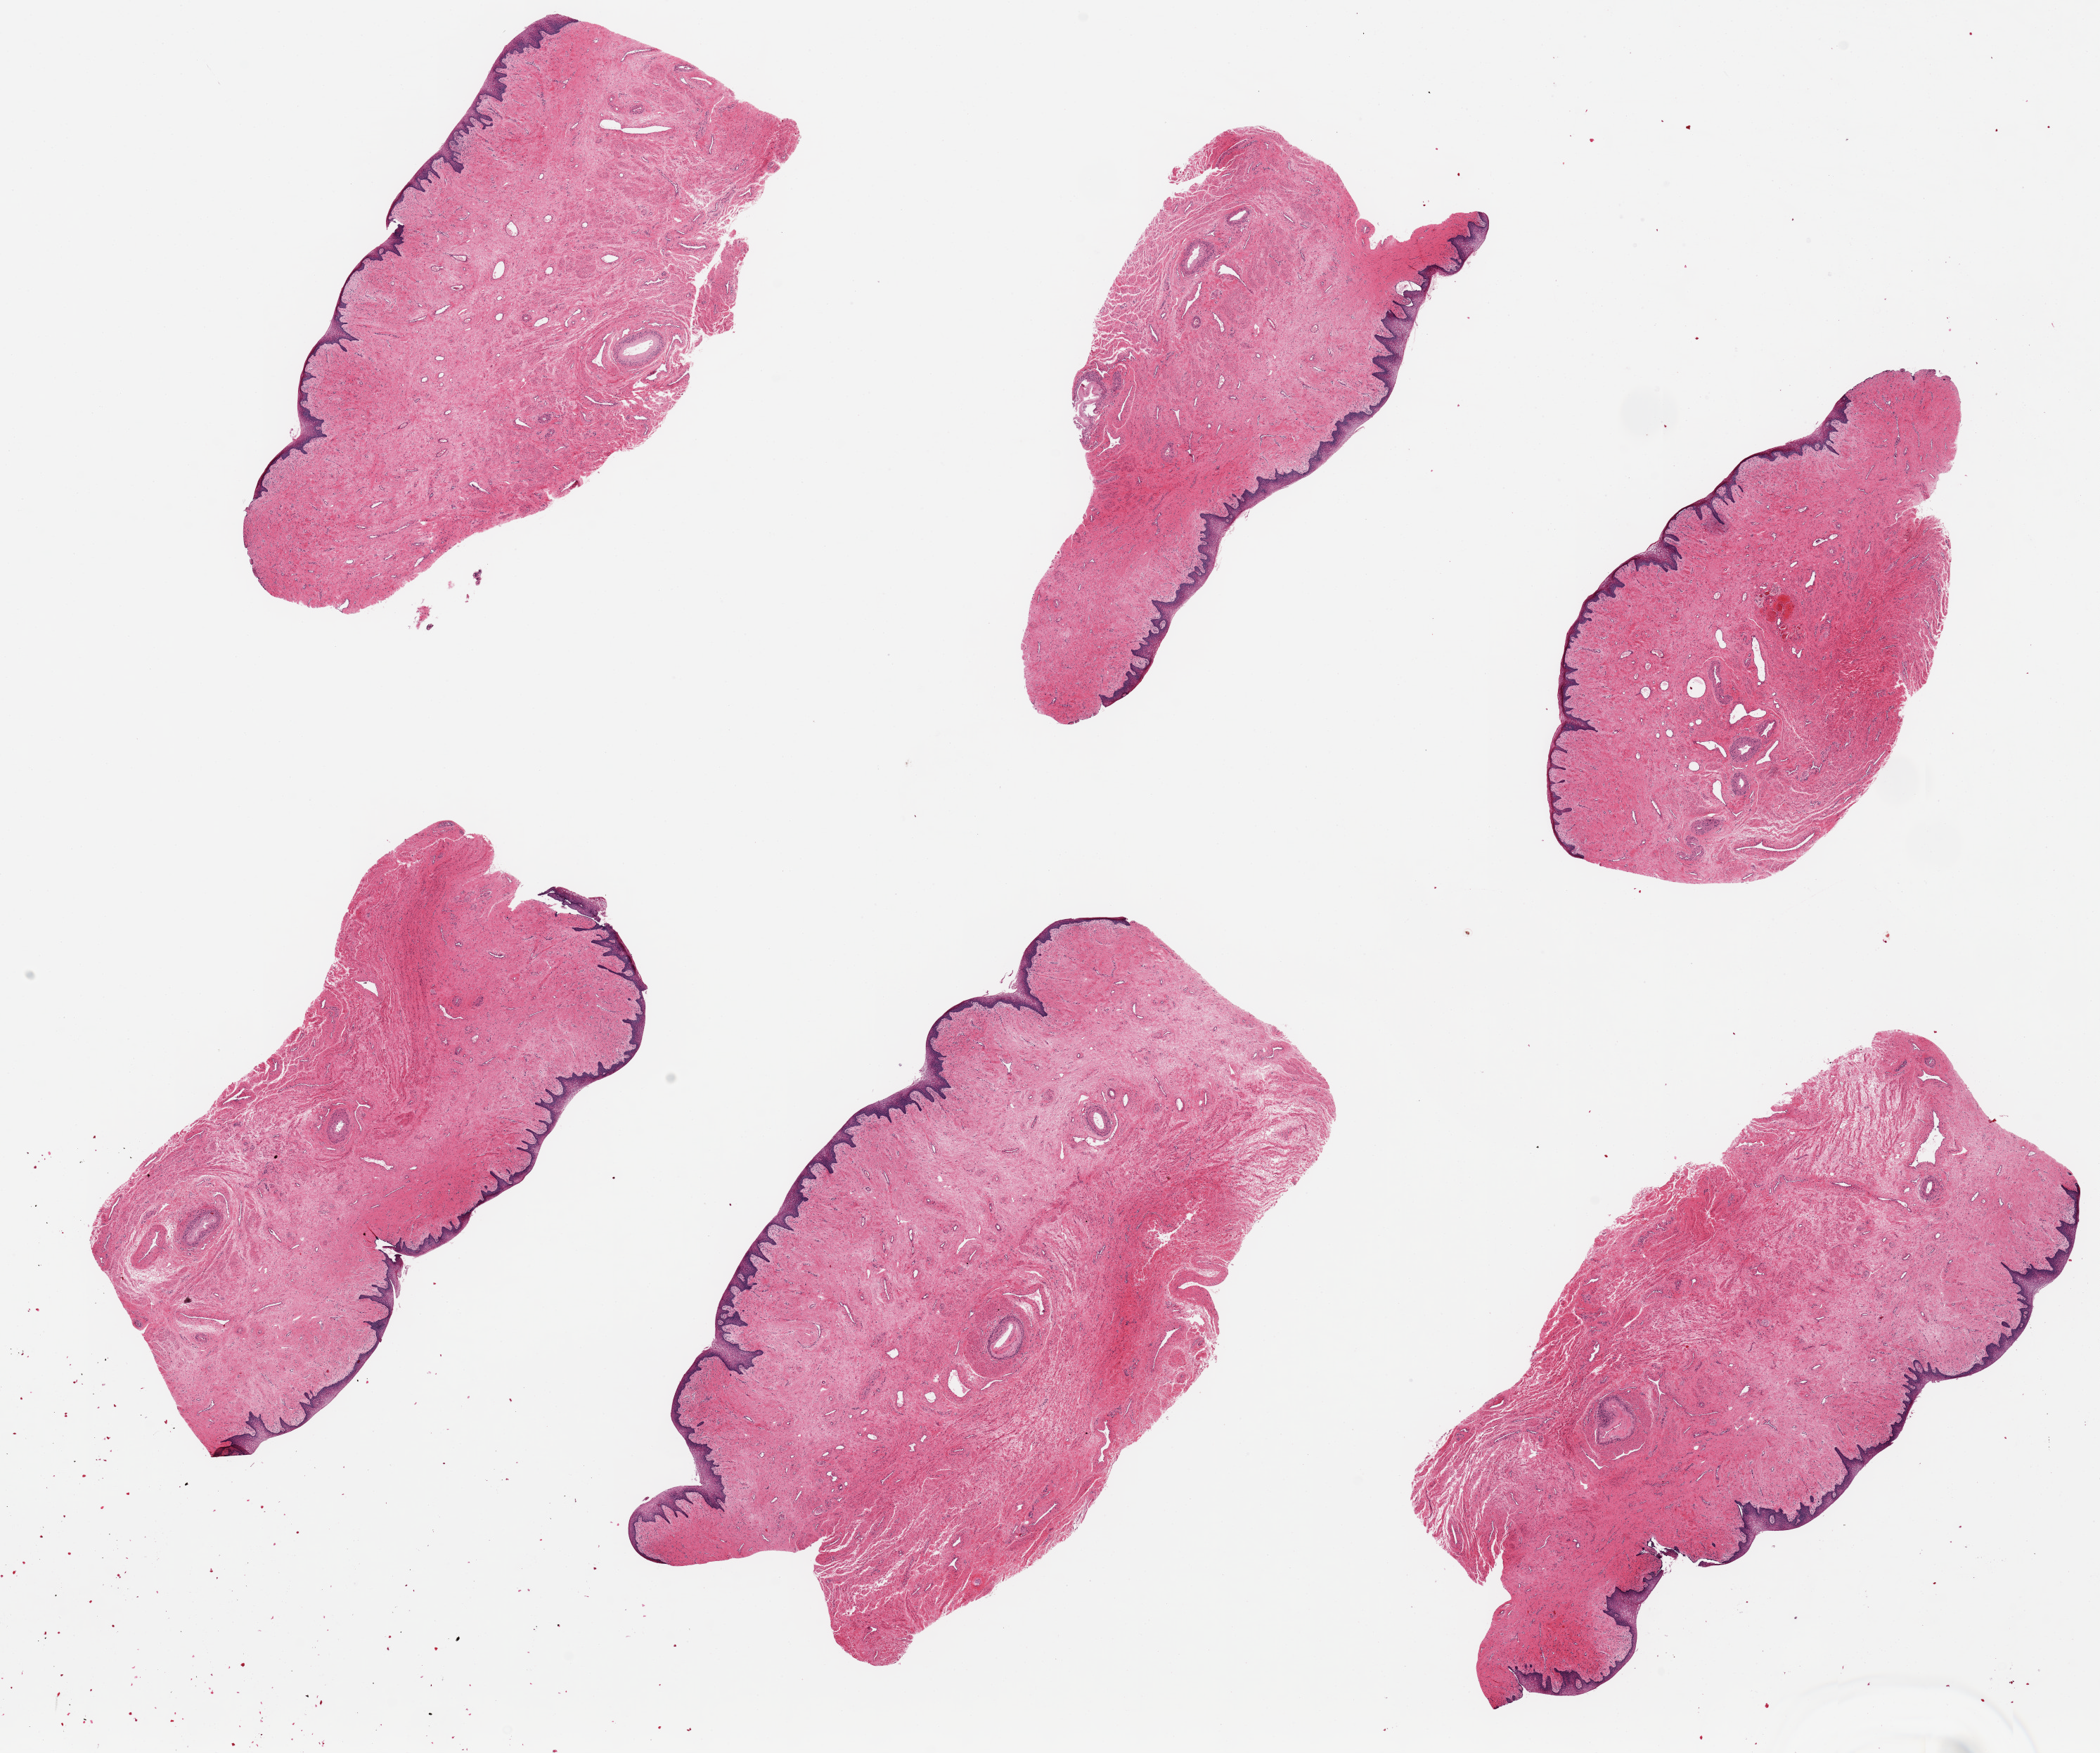
Whole-slide image, haematoxylin and eosin stain, brightfield, low-resolution overview of the scanned area, about 23.6 x 19.7 mm (slide scanned at 20x), PAXgene-fixed, paraffin-embedded tissue, section of vagina (target tissue), donor tissue sample. Female donor.
Reviewer comment on this tissue sample: 6 pieces, up to 5x8mm; well preserved.